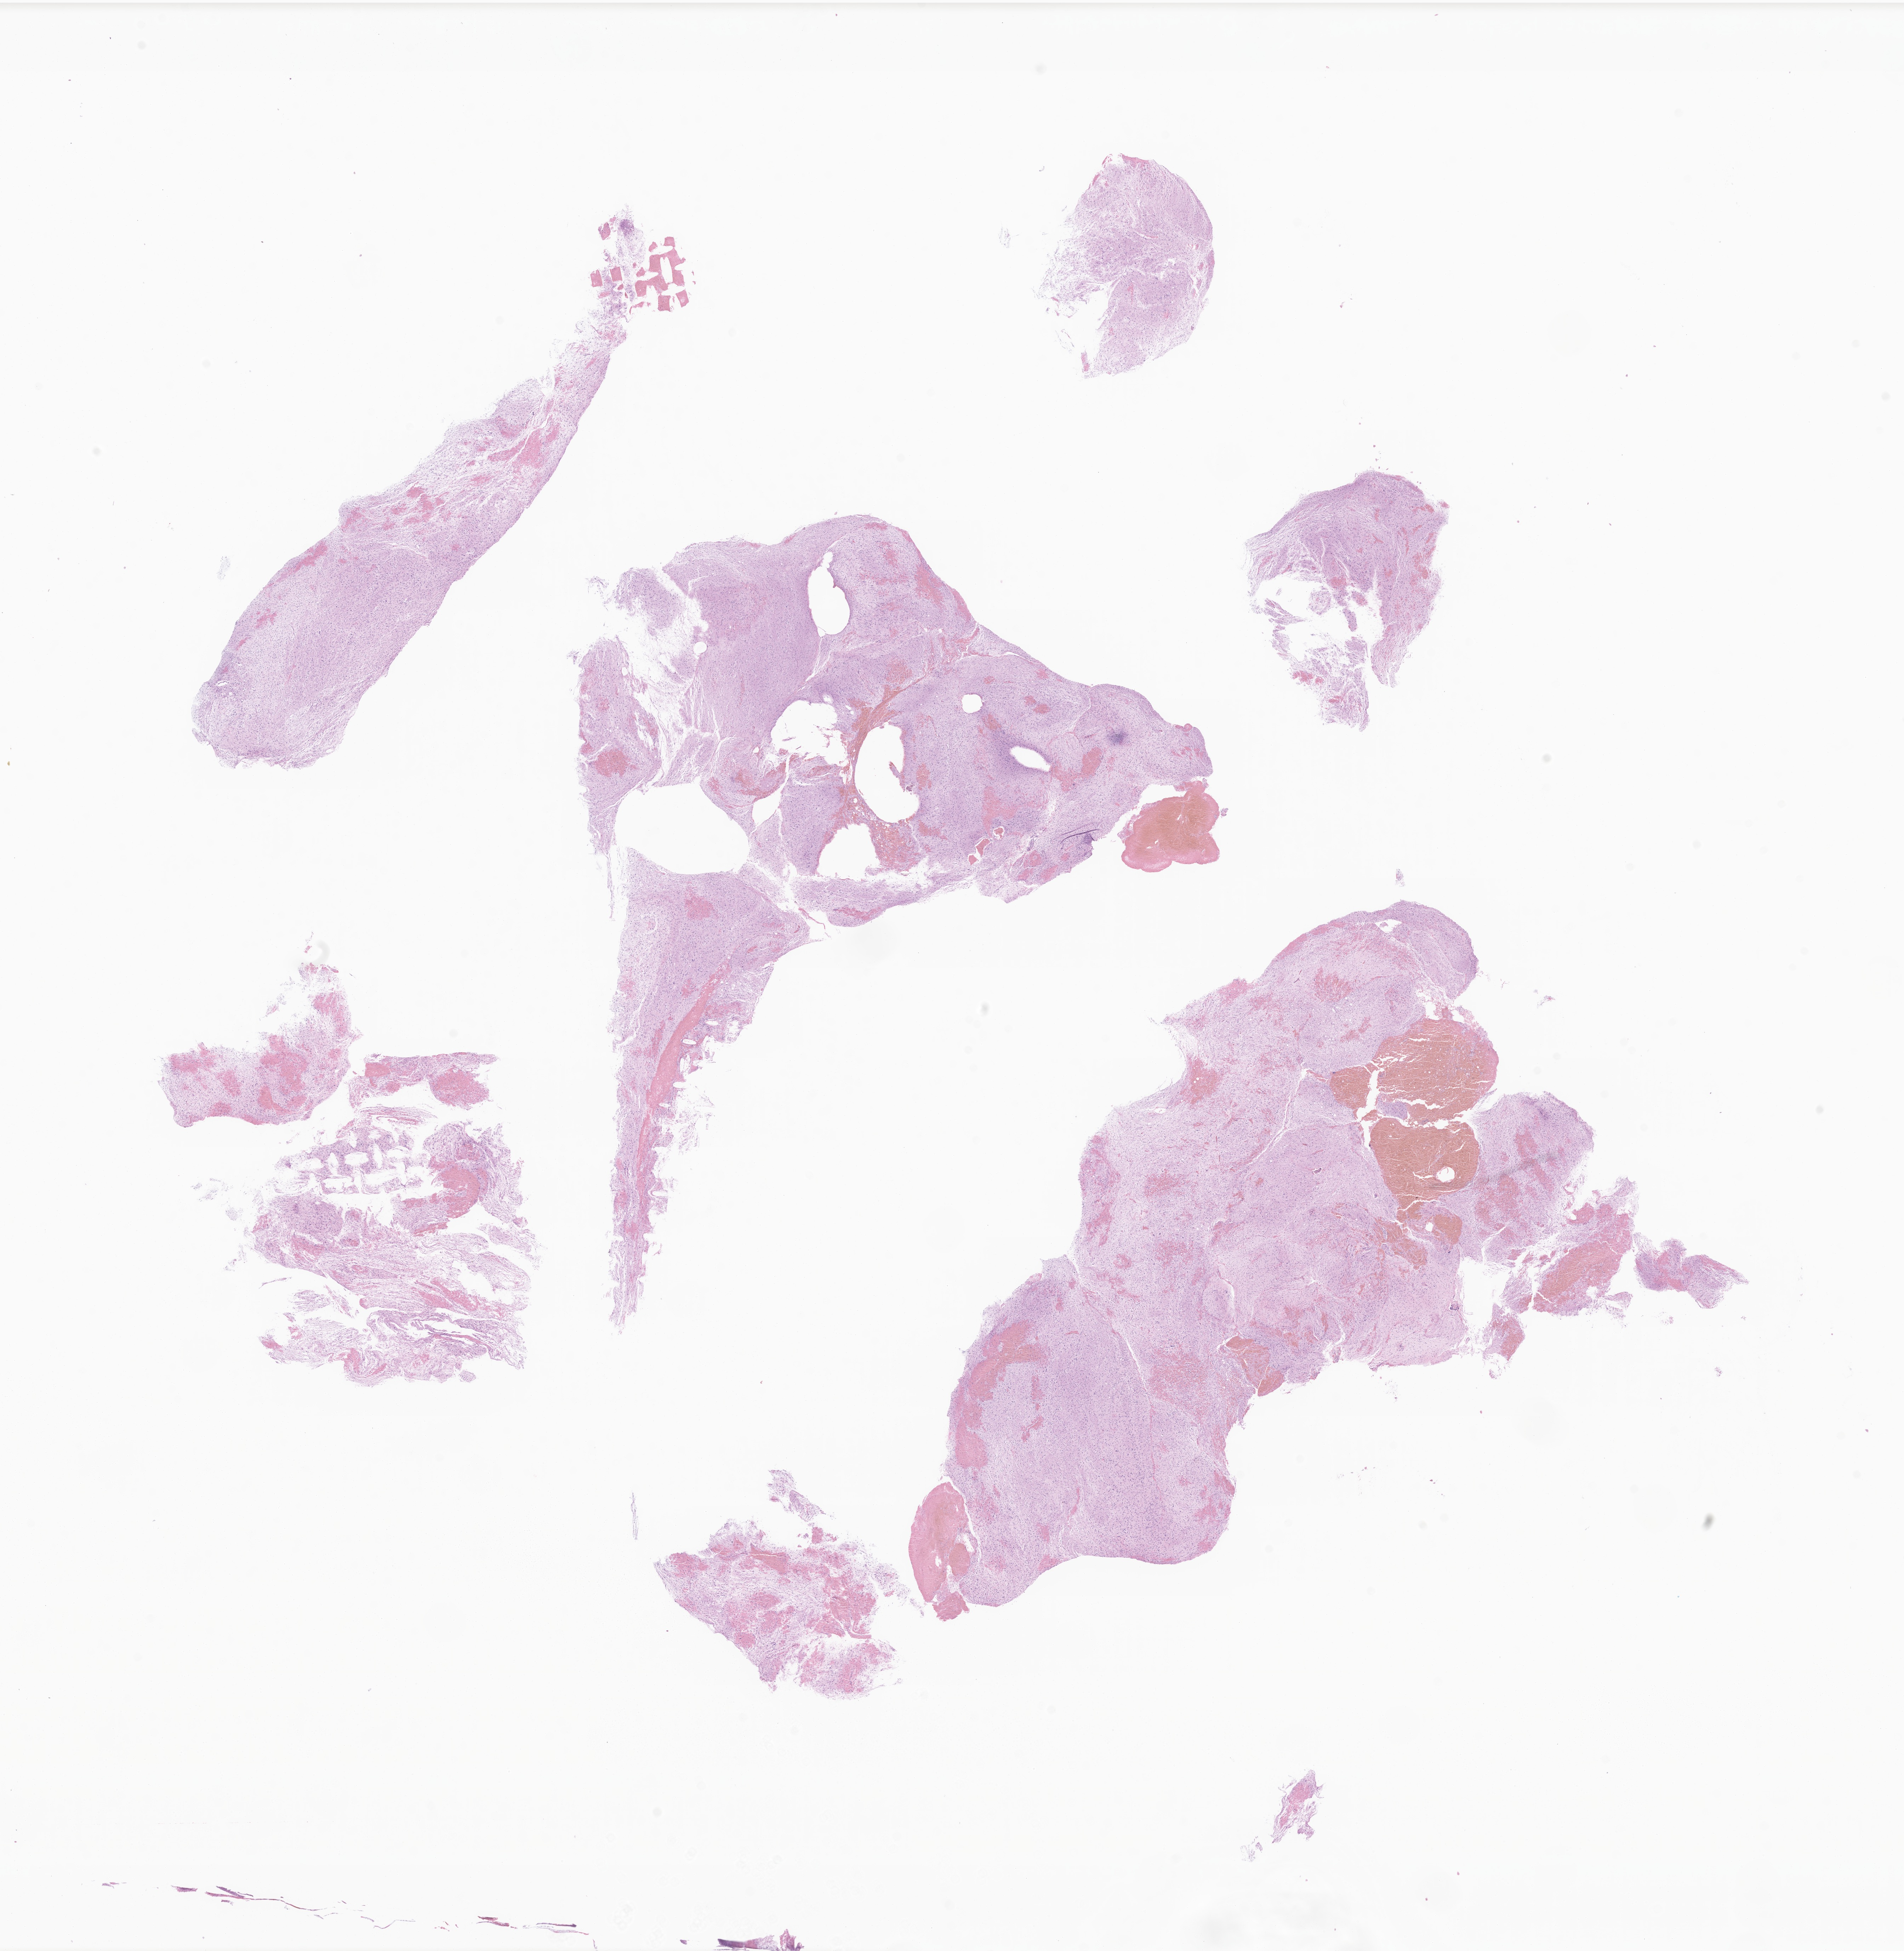
Digitized H&E-stained section of tumor tissue from the brain stem, low-resolution overview of the scanned area, about 22.7 x 23.2 mm; FFPE section. Male patient, age 257 months (21 years 5 months).
- recorded diagnosis: Astrocytoma, anaplastic, NOS